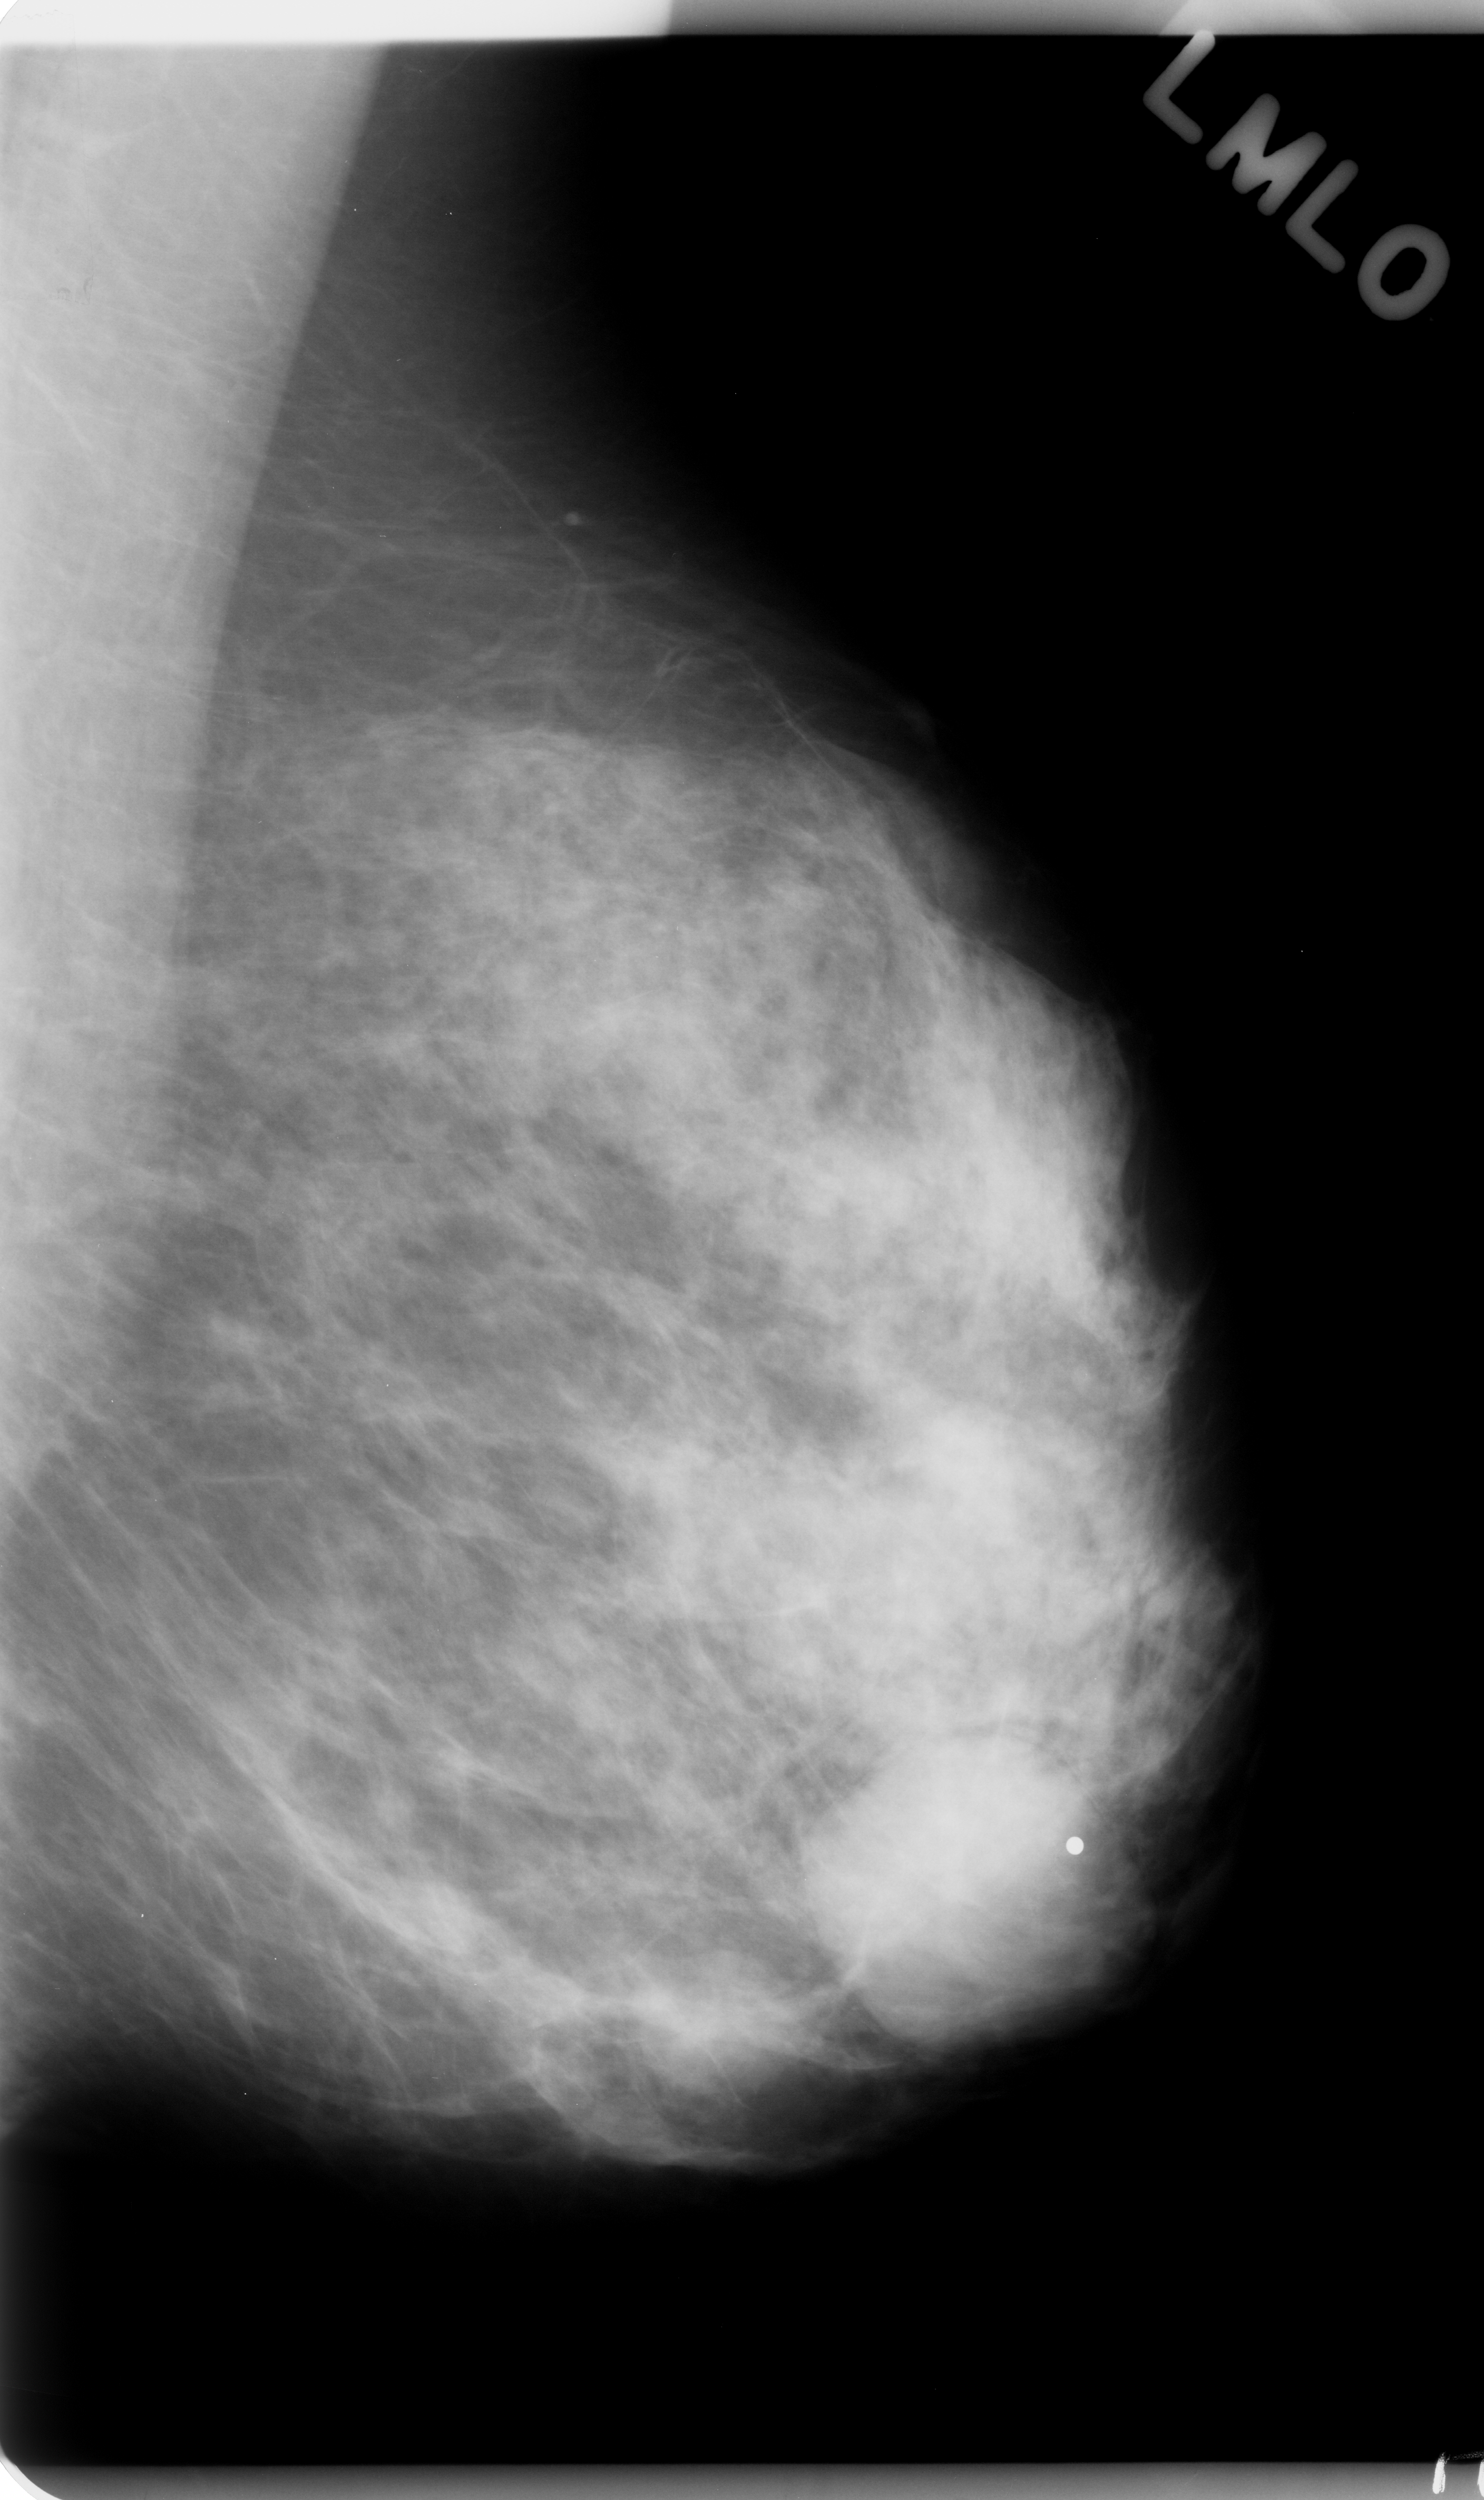
Mammogram (digitized film); left breast; mediolateral oblique (MLO) view; 1484 × 2500 image matrix.
Expert-marked regions of interest on this film, with their recorded descriptors:
- mass, shape round, margins circumscribed; BI-RADS assessment category 4; subtlety rating 3 on a 1 (subtle) to 5 (obvious) scale; pathology result (as recorded, not read from the image): benign: bounding box <621,1945,777,2097> (left, top, right, bottom; pixels)